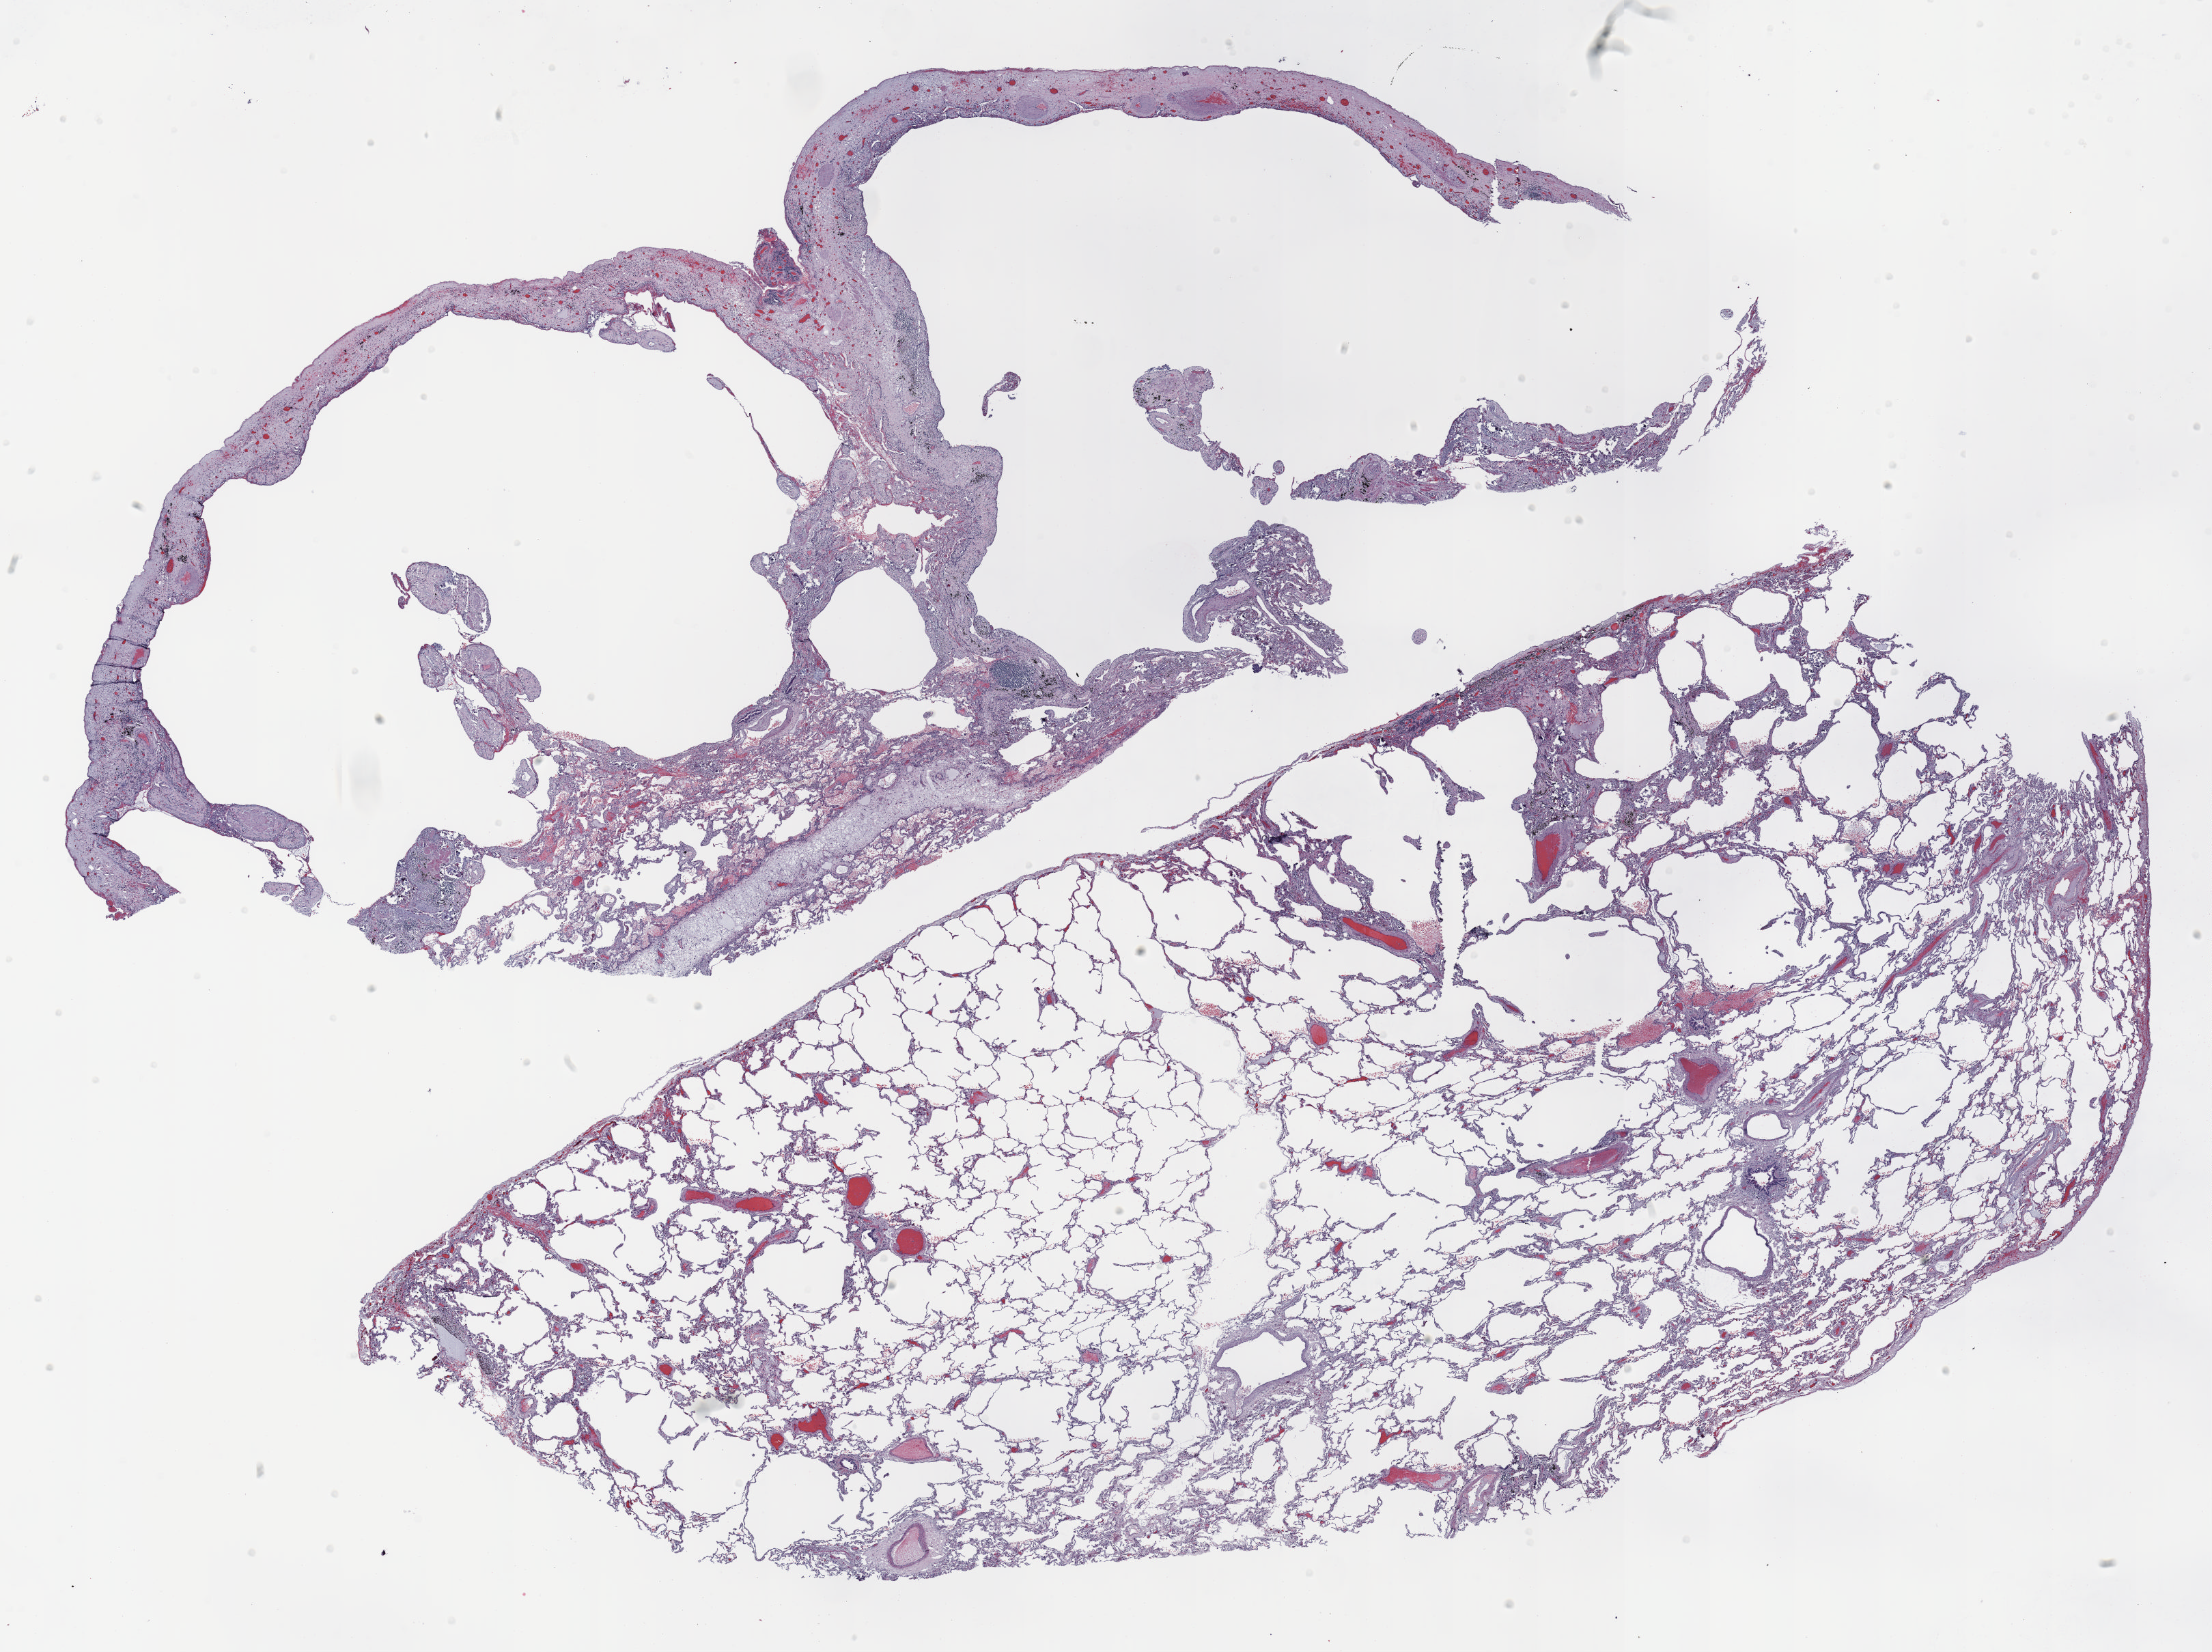
H&E-stained whole-slide image, low-resolution overview of the scanned area, about 26.0 x 19.4 mm. Formalin-fixed paraffin-embedded (FFPE) section. Lung tissue. Male, age 55 at enrolment. Grade: poorly differentiated (G3).
- ICD-O-3 topography: upper lobe of lung (C34.1)
- primary tumour location (clinical record): right upper lobe
- participant's lung-cancer diagnosis: Adenocarcinoma, NOS (ICD-O-3 8140/3)
- tumour size (pathology): 115 mm
- stage (AJCC 6th edition): IIB